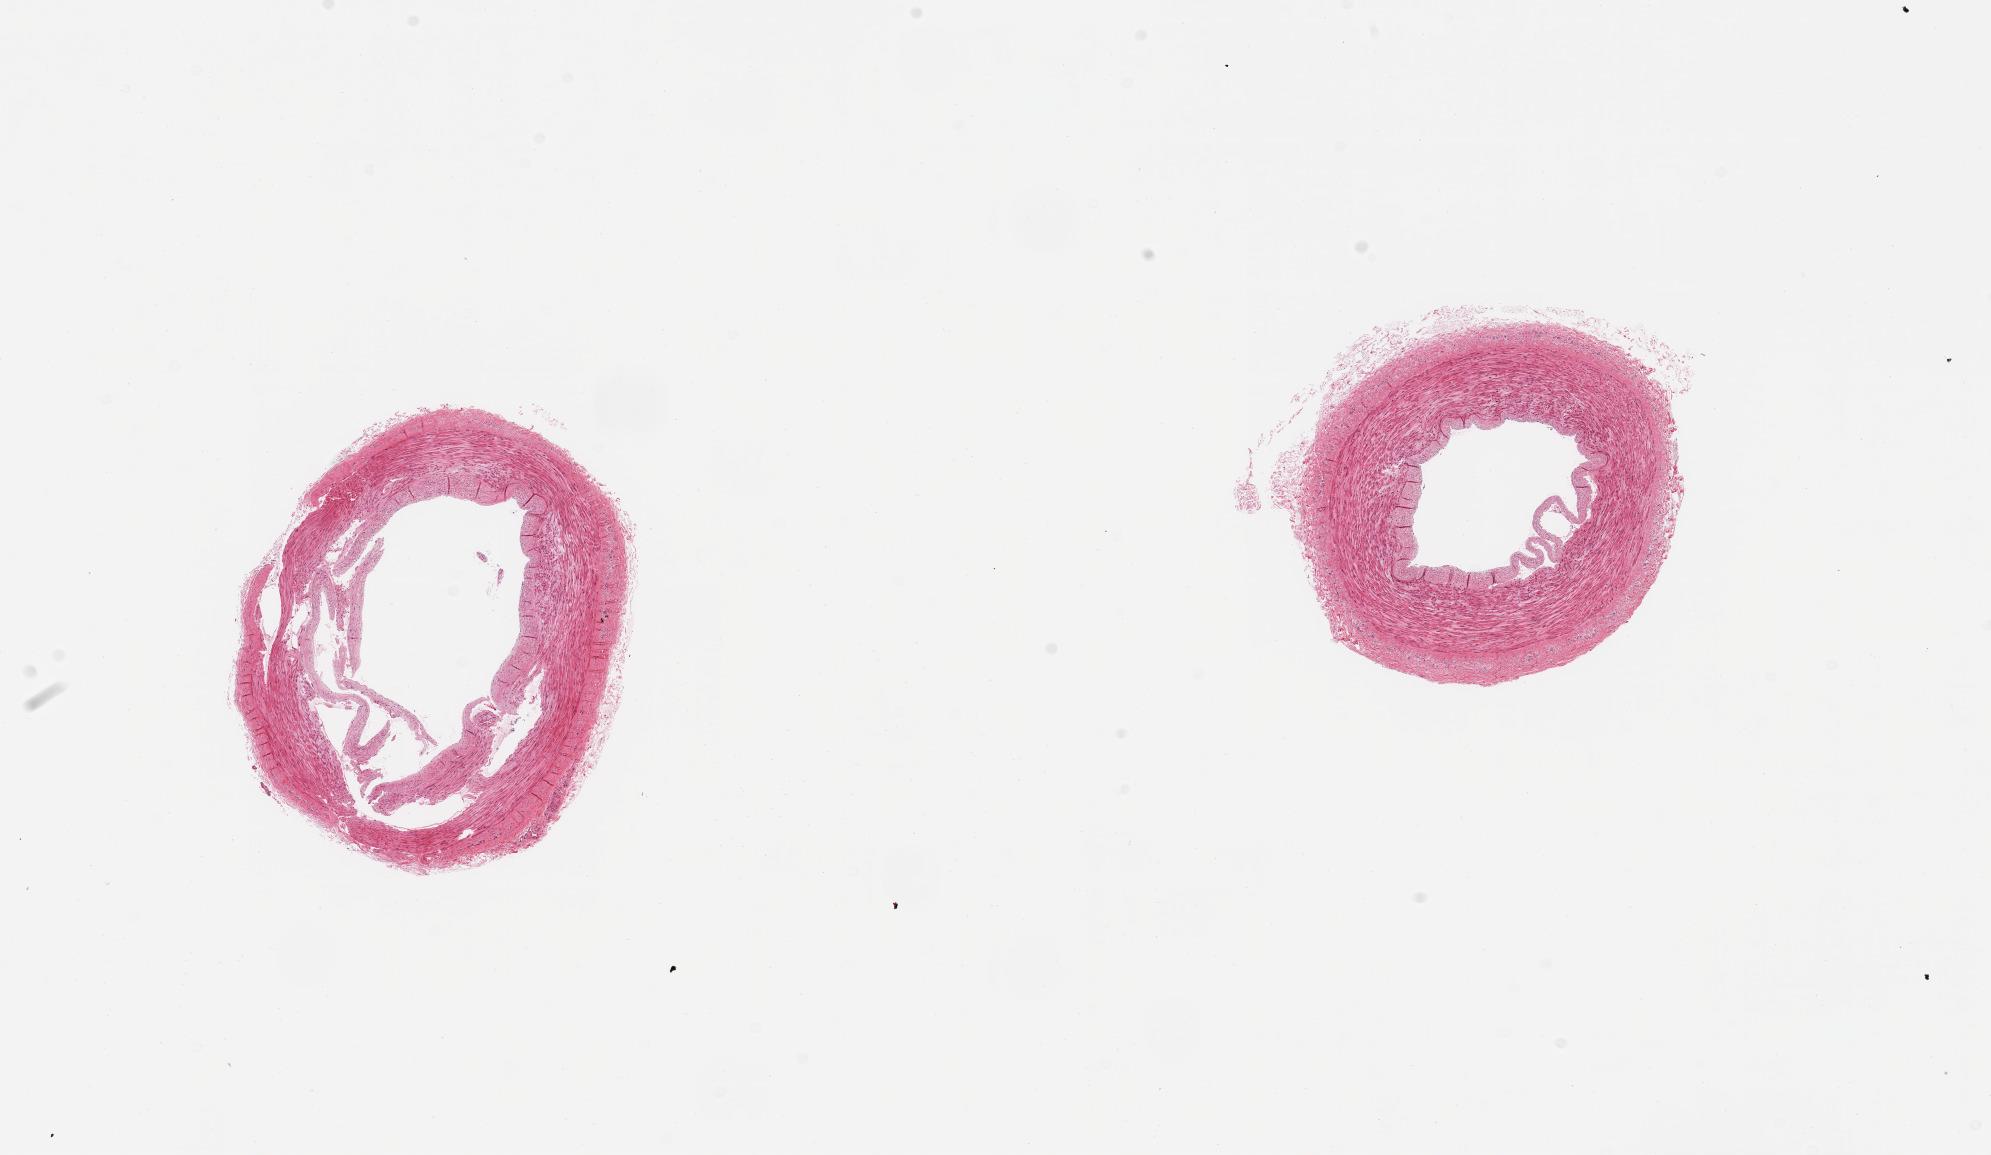
Whole-slide image, H&E stain, brightfield, shown as a low-resolution overview of the whole scanned area (about 15.8 x 9.1 mm, acquisition: 20x scan), PAXgene-fixed, paraffin-embedded tissue, sampled site (target tissue): tibial artery, tissue donor sample. Male donor.
Reviewer comment on this tissue sample: 2 pieces; 1 piece fragmented; minimal plaque.